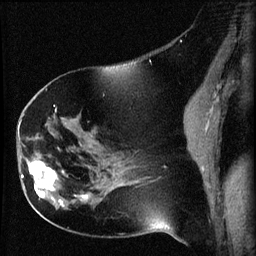
Breast MRI (dynamic contrast-enhanced), one sagittal slice; position 30 of 60 along the scan axis; dynamic contrast-enhanced series, image 2 of 3 at this slice position (ordered by acquisition); 1.5 T; TE 4.2 ms, TR 8.2 ms; 256 × 256 image matrix. Female patient, age 63 years.
Annotated regions visible in this slice (semi-automatically segmented with operator editing):
- analysis volume of interest (the breast-tissue region the enhancement analysis was run in; not a lesion): box from (x=22, y=156) to (x=64, y=202) px
- tumour enhancement mask (voxels above the 70 % enhancement threshold inside the analysis volume of interest): (x=22, y=159)–(x=64, y=202)